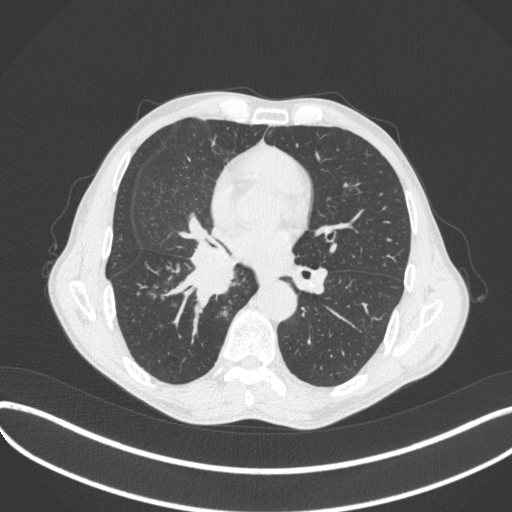
Chest CT, one axial slice. Position 216 of 481 along the scan axis. 120 kVp. Lung window (W 1500 / L -600 HU). 1 mm slice thickness. 512 × 512 image matrix. Male patient, age 65 years. From the clinical record (not read from this slice): clinical TNM (as recorded): T2a N0 M0; histopathological grade: G2.
Outlined on this slice (rectangle marked by the reading radiologist):
- lung tumour (recorded histology: squamous cell carcinoma): box from (x=168, y=241) to (x=237, y=303) px